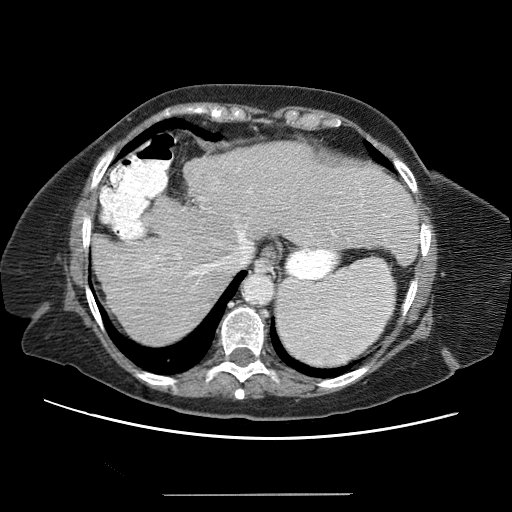
Contrast-enhanced abdominal CT (liver protocol), one axial slice. Slice 48 of 65 in the series (ordered by position). Soft-tissue window (W 400 / L 40 HU). 512 × 512 image matrix, field of view 380 × 380 mm. Case-level facts recorded for this patient, not image findings: diagnosis: hepatocellular carcinoma (patient treated with transarterial chemoembolisation; whether this scan precedes or follows treatment is not stated here); TNM stage (as recorded): Stage-IIIB; Child-Pugh class: A; tumour nodularity: uninodular.
Outlined on this slice (semi-automatically segmented with operator editing):
- liver parenchyma outside the tumour (the mass and vessels are separate outlines, so this box may not span the whole liver): bounding box <92,144,416,339> (left, top, right, bottom; pixels)
- mass: <140,243,184,287>
- liver vessels: <96,169,397,315>